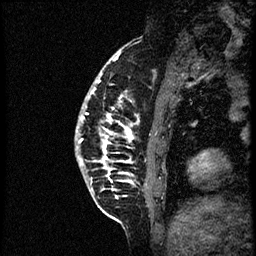
Breast MRI (dynamic contrast-enhanced), one sagittal slice. Slice 14 of 56 in the series (ordered by position). Dynamic contrast-enhanced study with each time point stored as its own series, time point 2 of 3 at this slice position (early post-contrast, ordered by acquisition time). 1.5 T. TE 4.2 ms, TR 21.3 ms. 2 mm slice thickness. 256 × 256 image matrix. Patient: female, 41 years. From the clinical record (not read from this slice): setting: breast cancer imaged before/during neoadjuvant chemotherapy; receptor status: HER2-positive.
Annotated regions visible in this slice (semi-automatic segmentation, software-assisted and operator-edited):
- analysis volume of interest (the breast-tissue region the enhancement analysis was run in; not a lesion): box from (x=74, y=73) to (x=177, y=205) px
- tumour enhancement mask (voxels above the 100 % enhancement threshold inside the analysis volume of interest): (x=79, y=76)–(x=133, y=178)